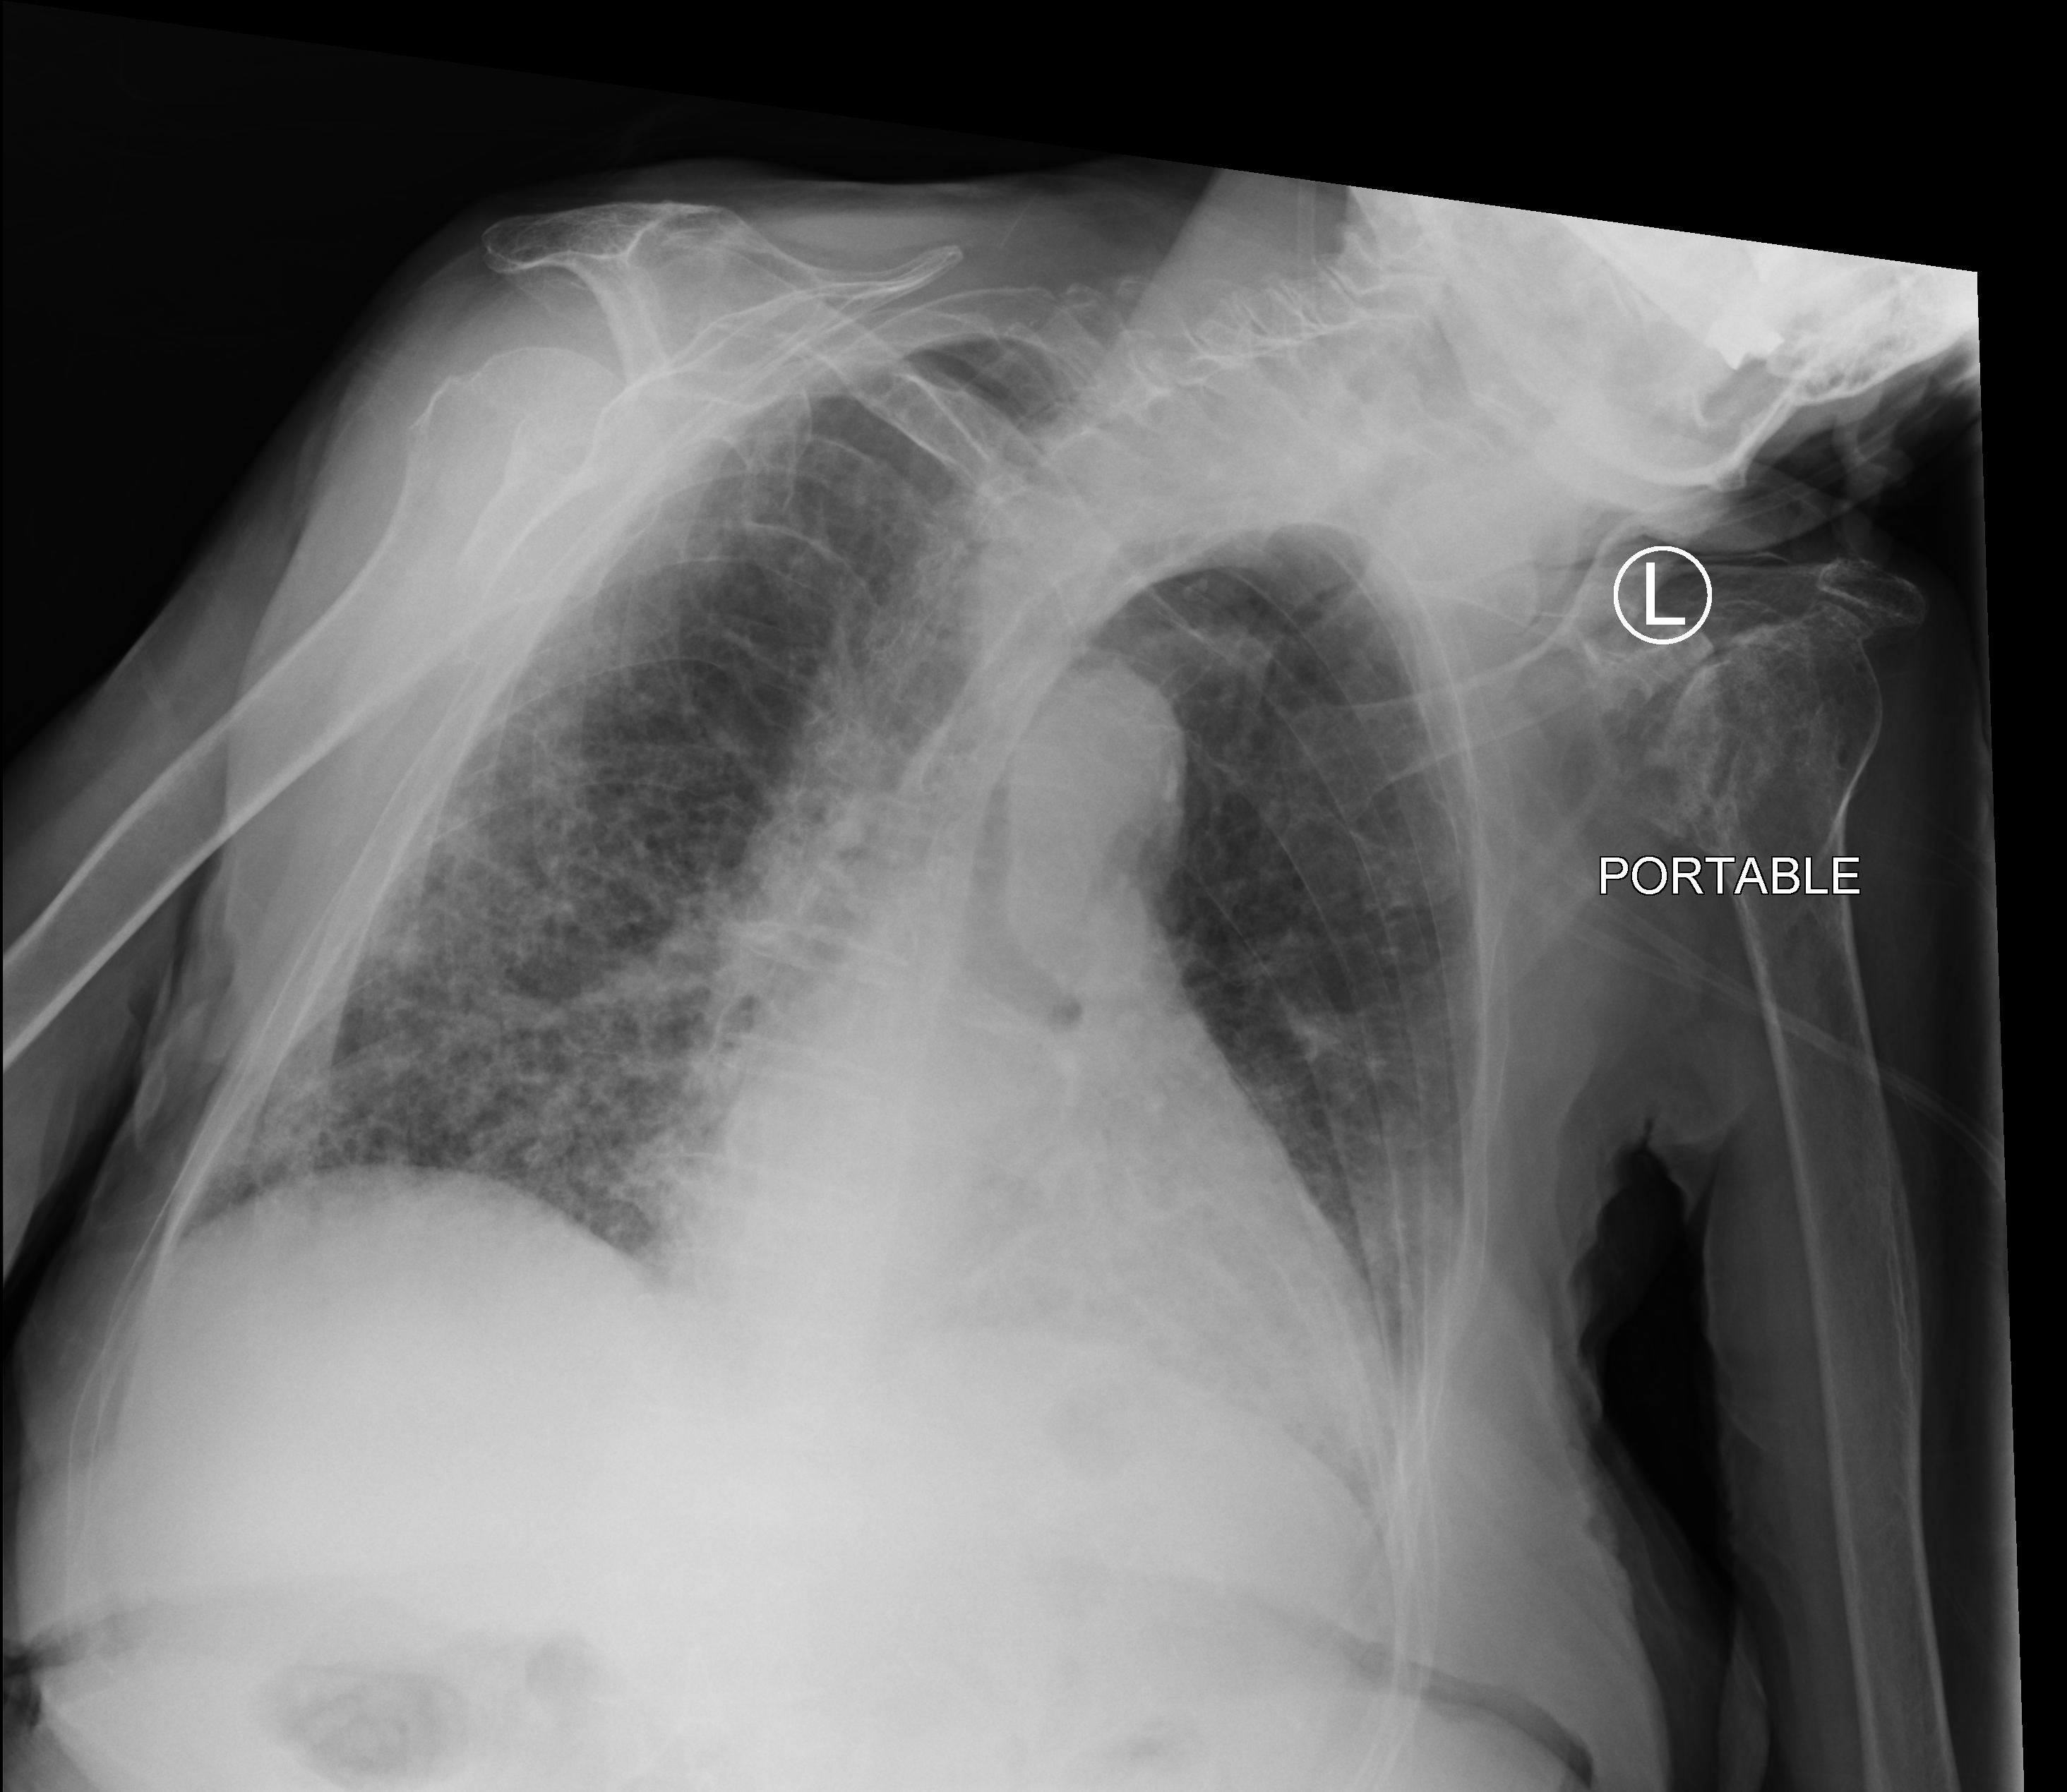
Bedside chest radiograph (computed radiography); anteroposterior (AP) projection. Female patient hospitalised with COVID-19, age 75–90 years.
Admission-level facts for this patient (not findings on this image; timing relative to this image not recorded):
- admitted to intensive care during this hospital stay: no